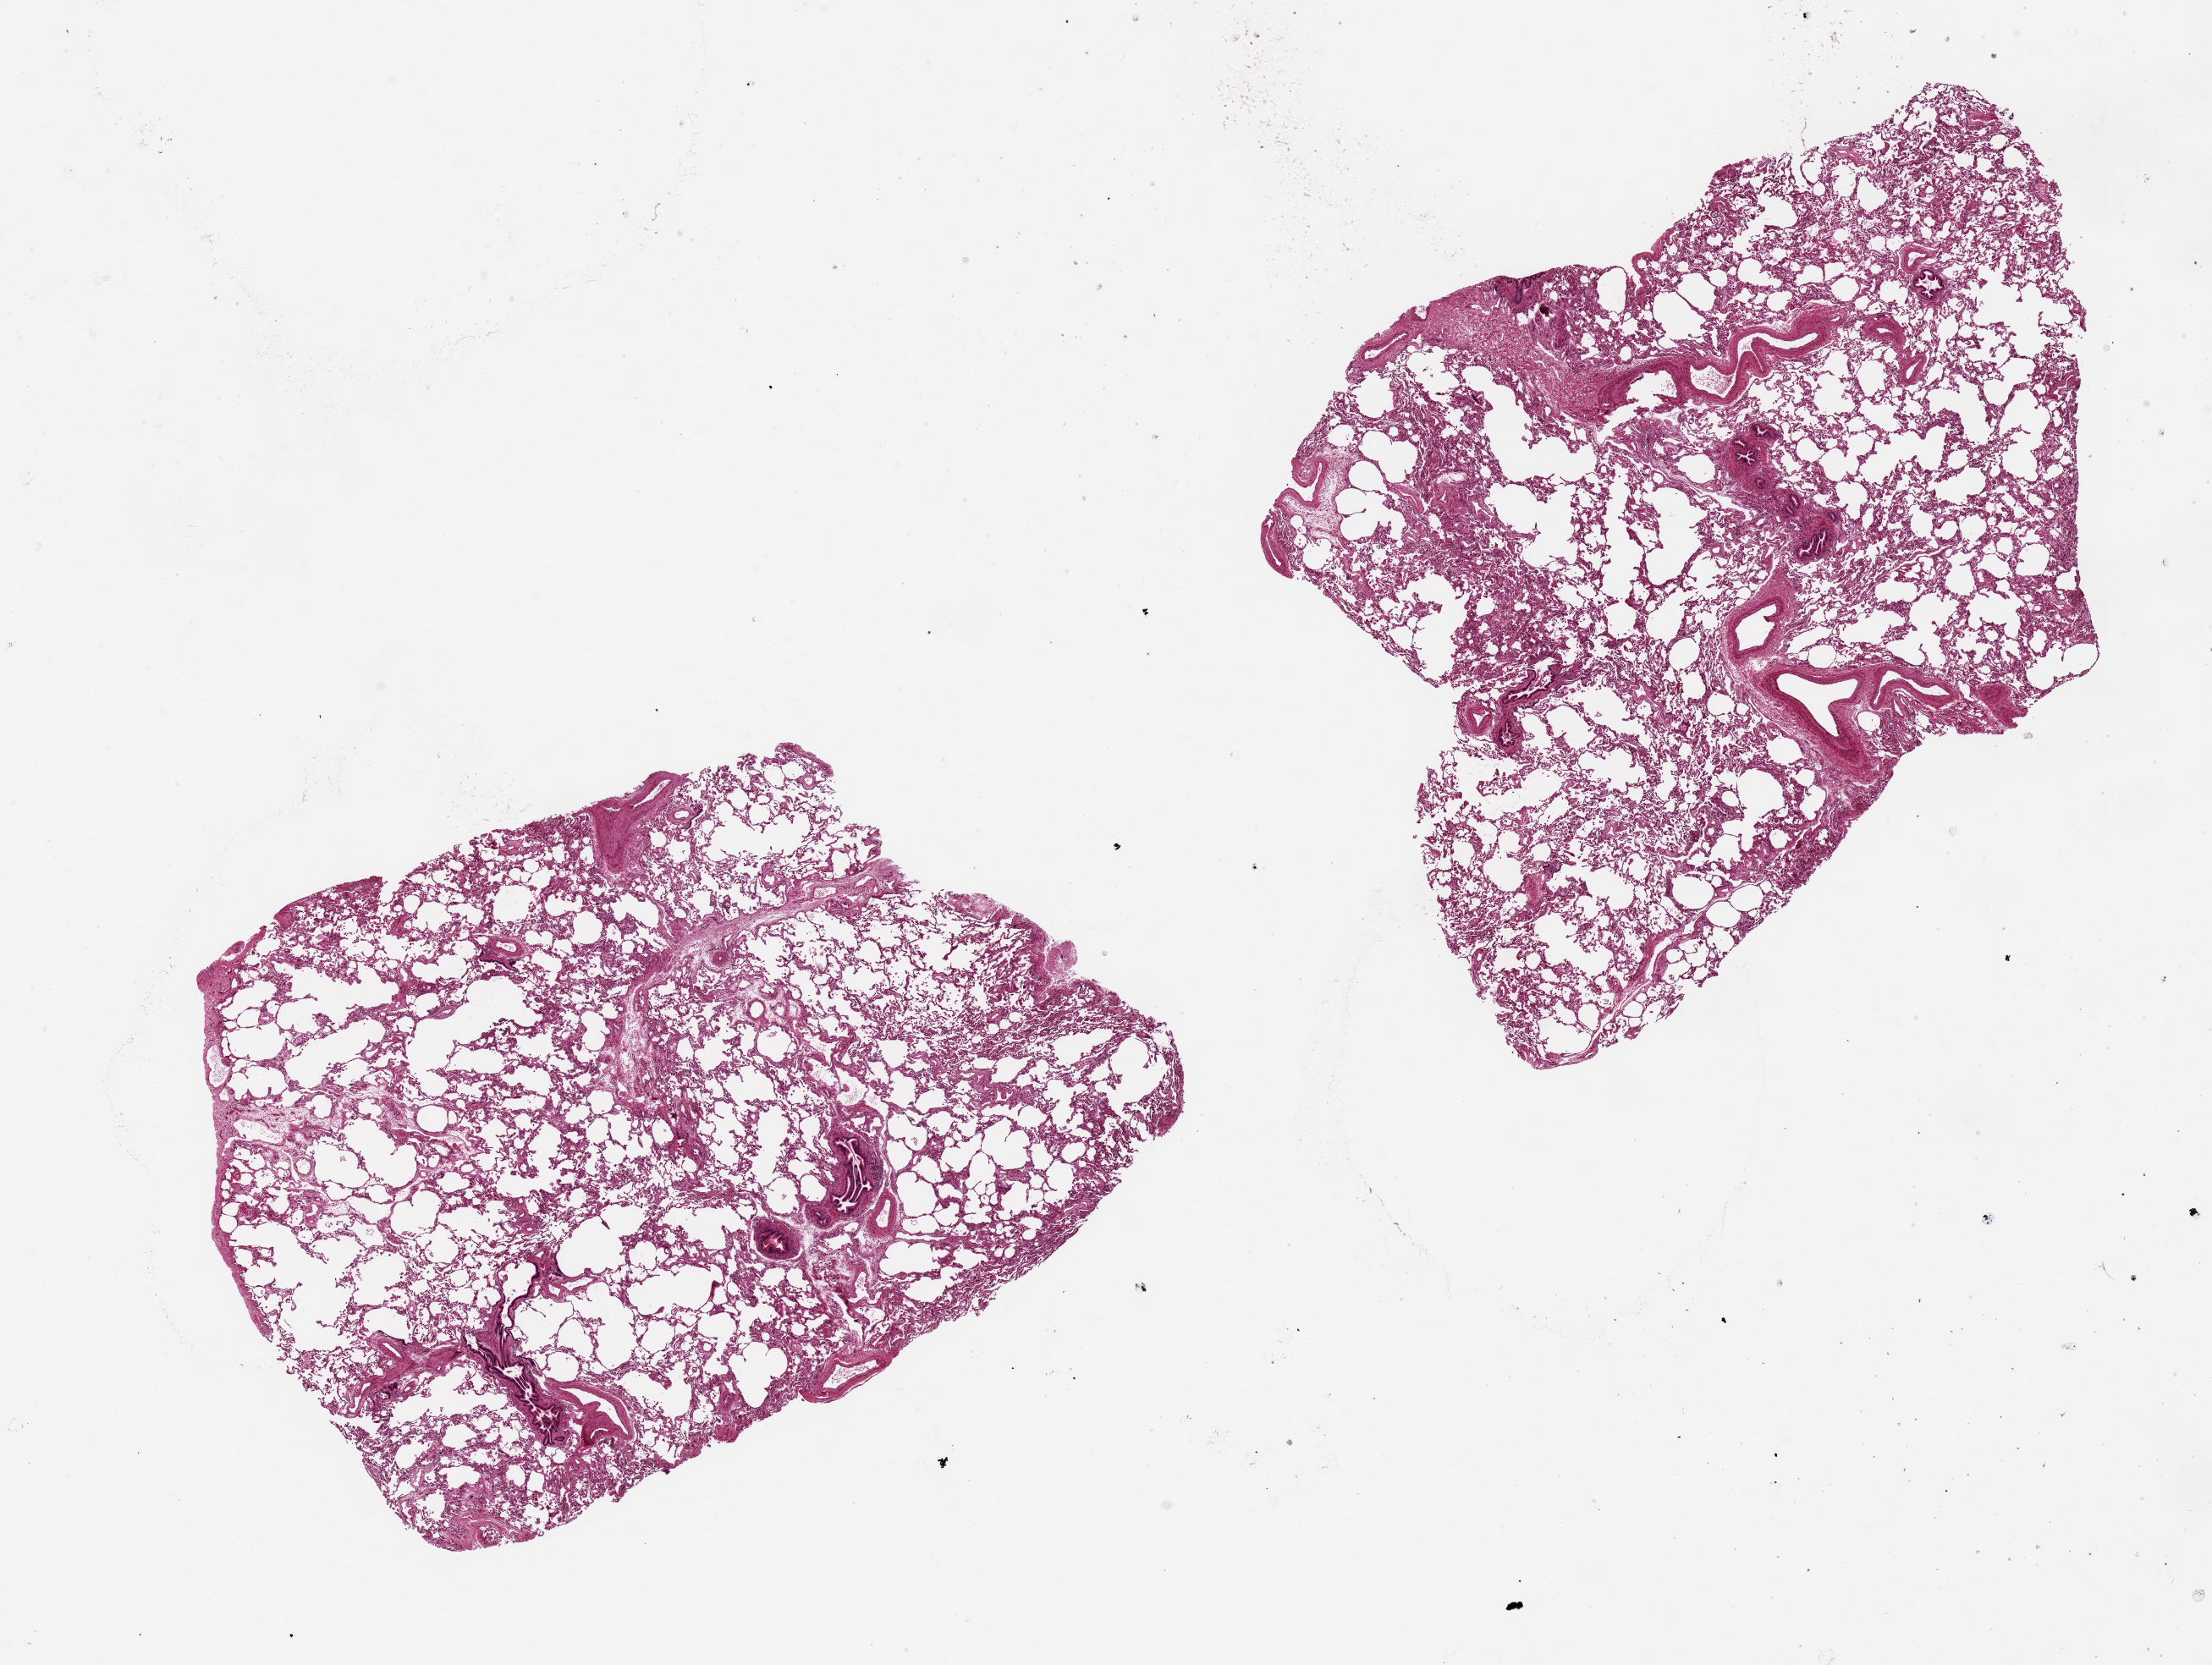
Digitized hematoxylin and eosin (H&E)-stained section — low-resolution overview of the scanned area, about 20.7 x 15.6 mm (acquisition: 20x scan), PAXgene-fixed, paraffin-embedded tissue, sampled site (target tissue): lung, tissue donor sample. Donor sex: female.
Reviewer comment on this tissue sample: 2 pieces ~7x5mm; Minimal congestion/edema; bronchial mucosa remarkably well preserved.